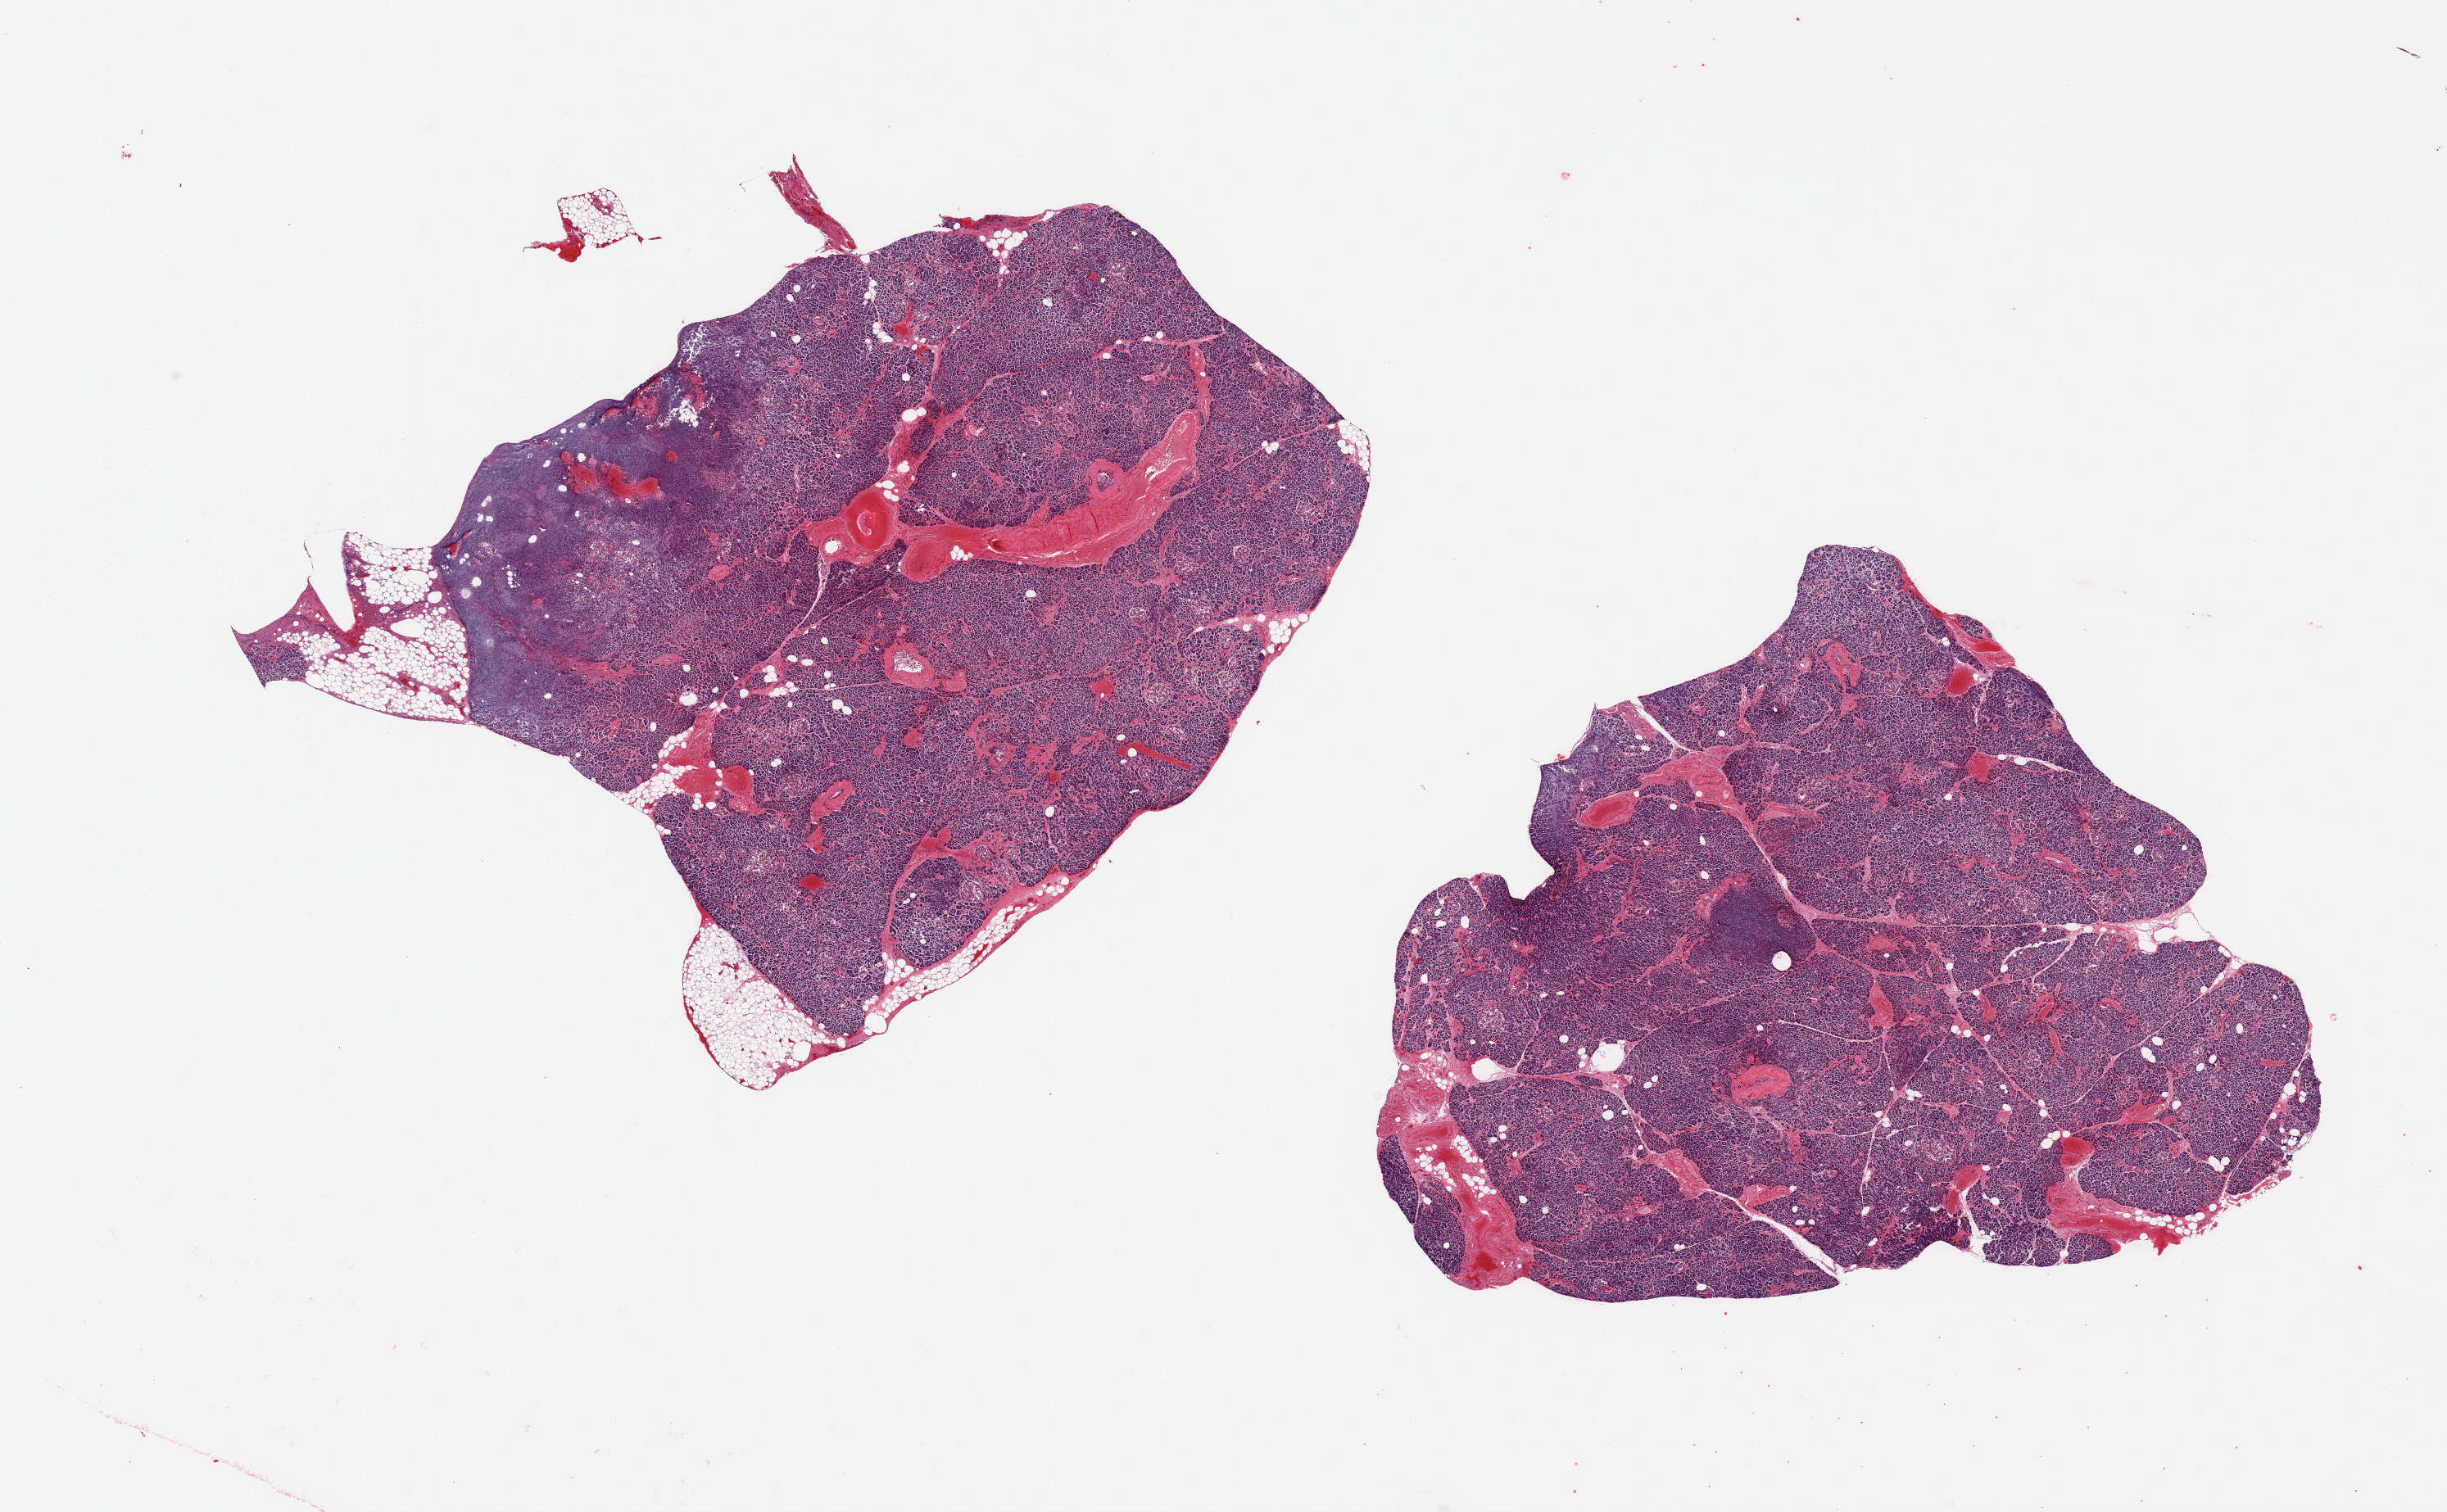
Whole-slide image, hematoxylin and eosin (H&E) stain, brightfield — shown as a low-resolution overview of the whole scanned area (about 23.6 x 14.6 mm, from a 20x scan). PAXgene-fixed paraffin-embedded (PFPE) section. Section of pancreas (target tissue). Tissue donor sample. Female donor.
* reviewer comment on this tissue sample: 2 pieces: 5% external fat on 1